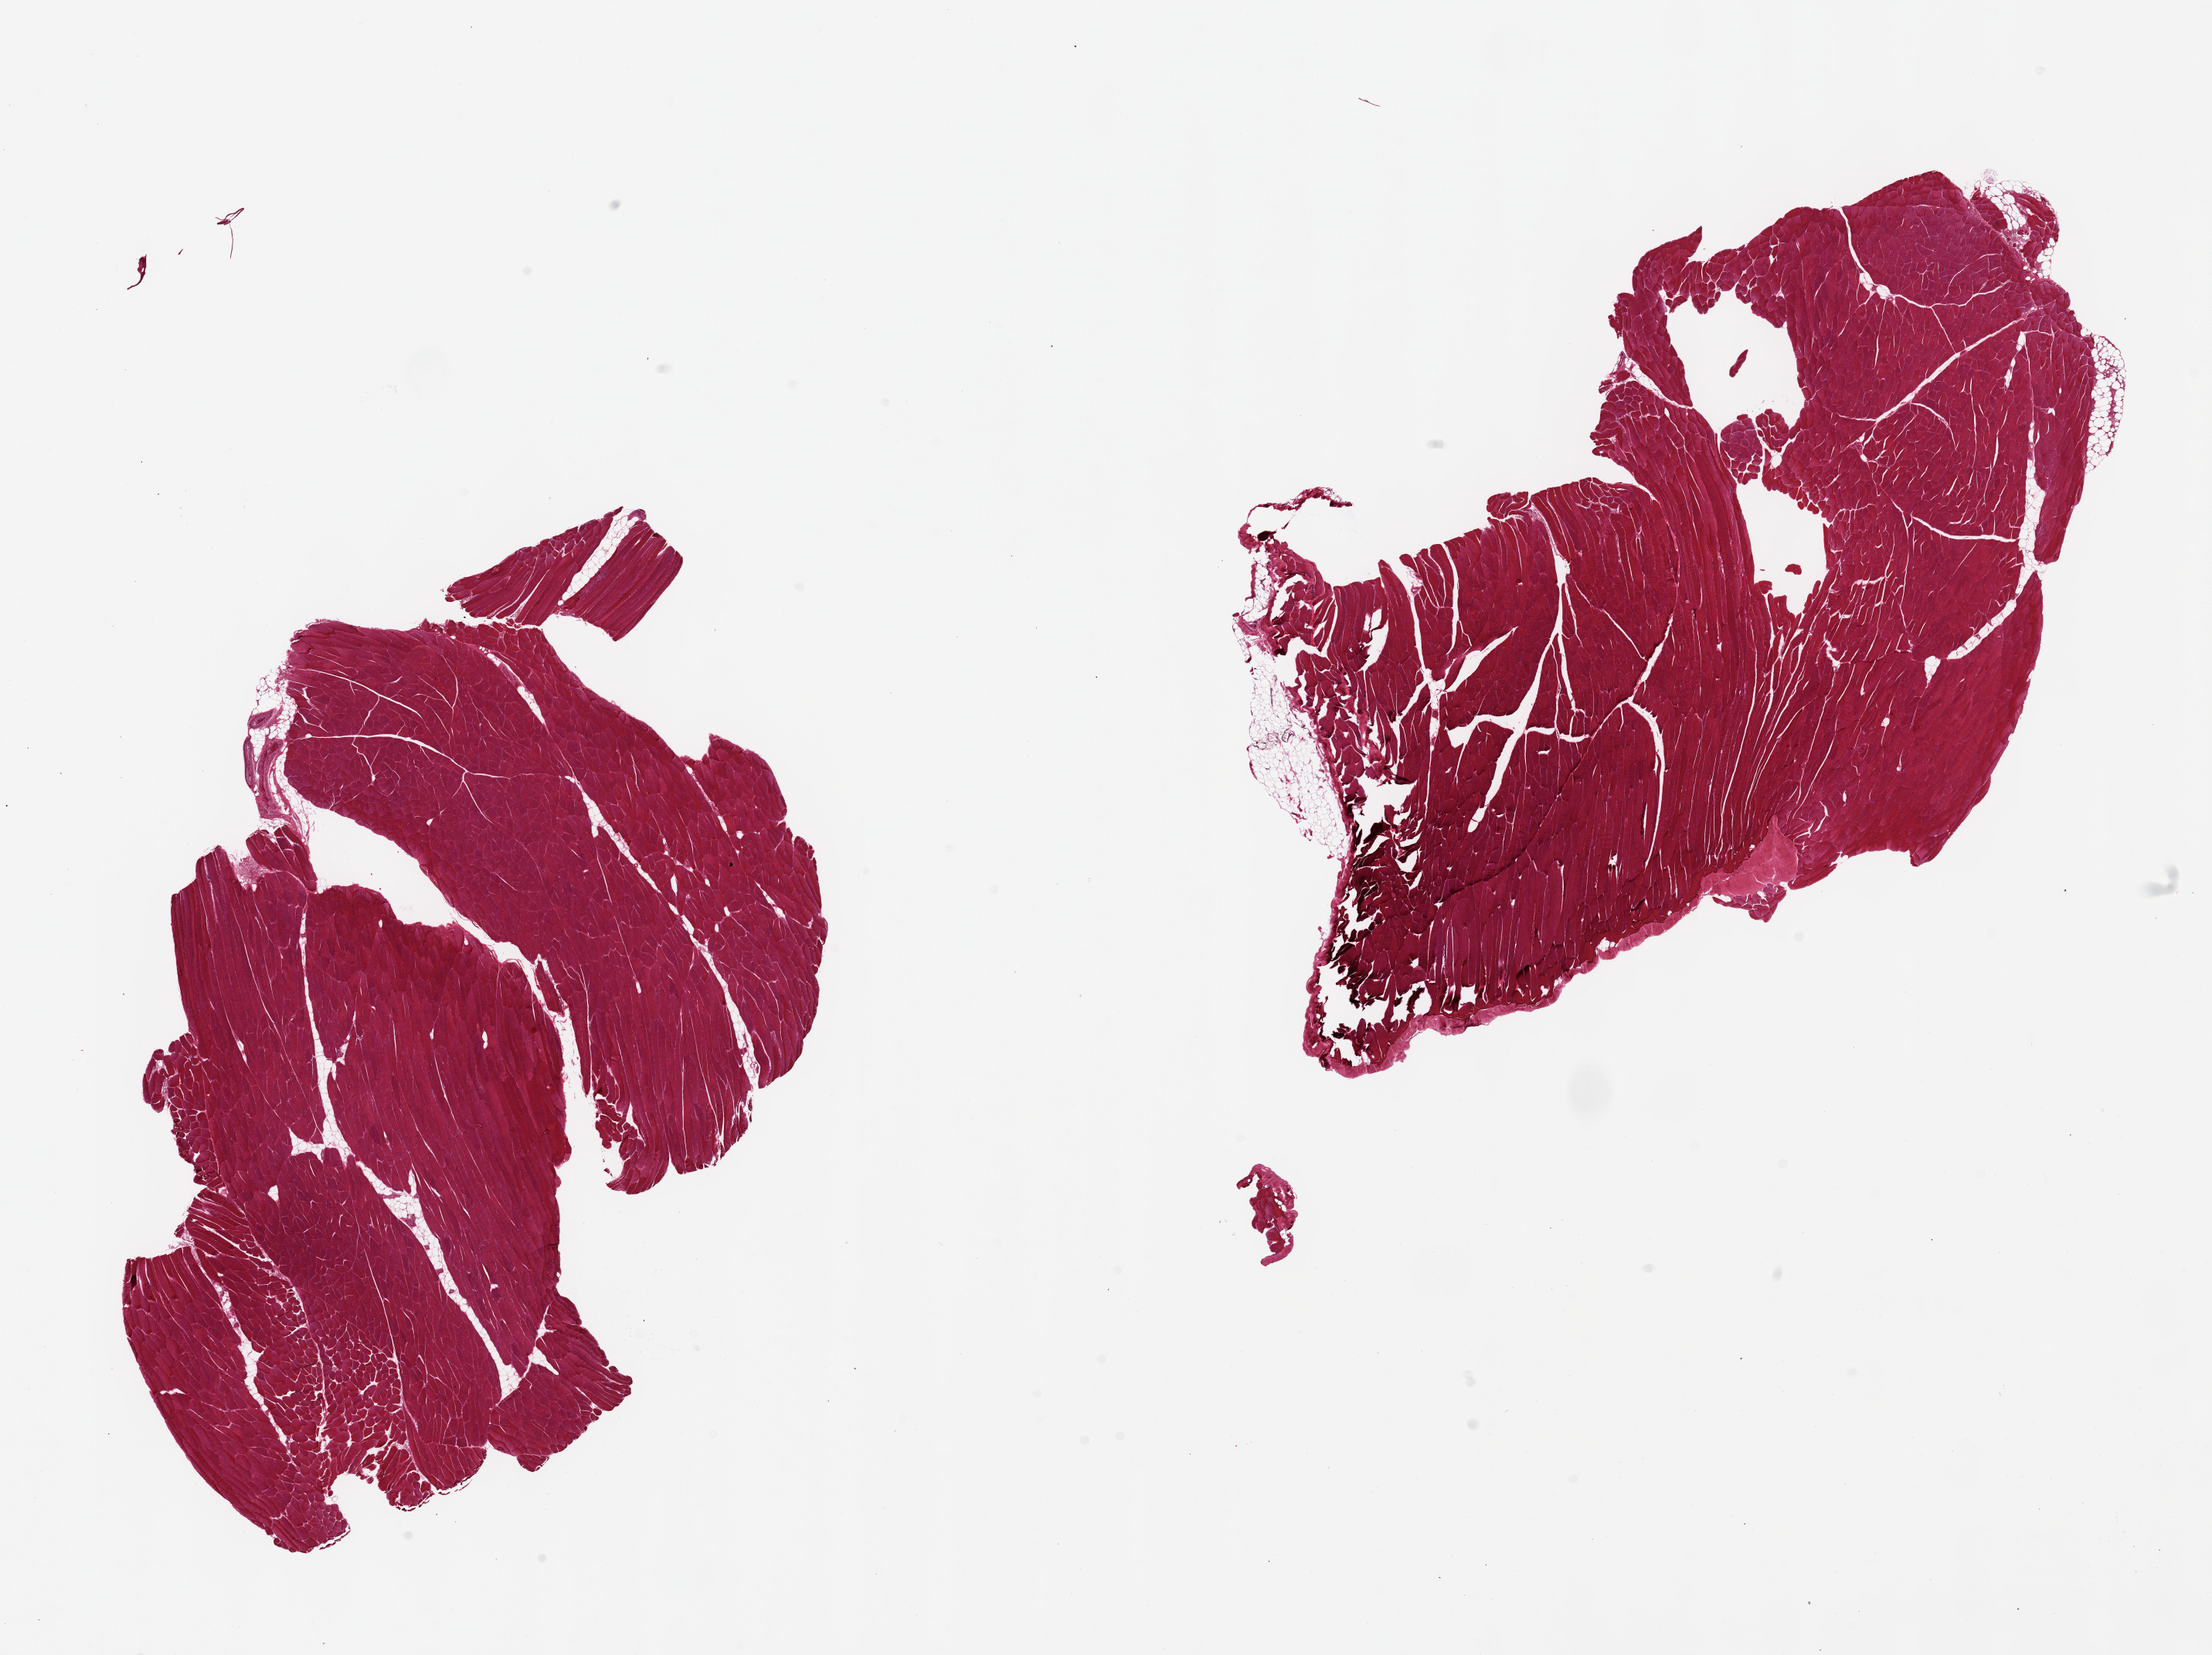
Digitized hematoxylin and eosin (H&E)-stained section, whole scanned area (about 22.6 x 16.9 mm) shown as a low-resolution overview. PAXgene-fixed, paraffin-embedded tissue. Section of skeletal muscle (target tissue). Tissue donor sample.
Pathologist's review note for this sample: 2 pieces.